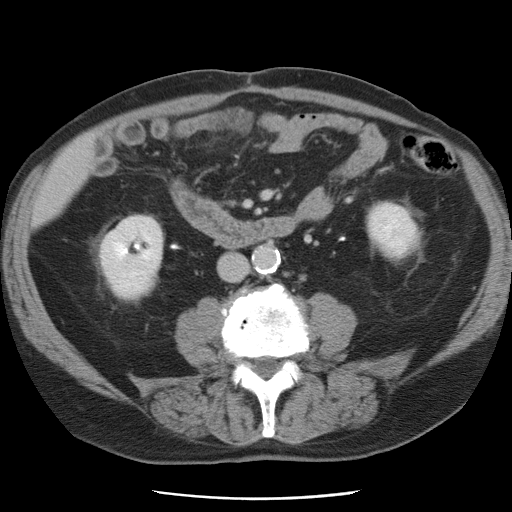
Contrast-enhanced abdominal CT, one axial slice. Position 14 of 78 along the scan axis. 120 kVp. Intravenous contrast given. Soft-tissue window (W 400 / L 40 HU). 5 mm slice thickness. 512 × 512 image matrix. Male patient, age 75 years. Case-level facts recorded for this patient, not image findings: diagnosis: colorectal cancer liver metastases, imaged before liver resection; multiple liver metastases: yes; largest metastasis: 2.4 cm; chemotherapy before resection: yes.
Annotated regions visible in this slice (manually delineated by an expert):
- liver: bounding box <35,139,92,224> (left, top, right, bottom; pixels)
- planned liver remnant (the part of the liver to remain after resection): <35,139,92,224>